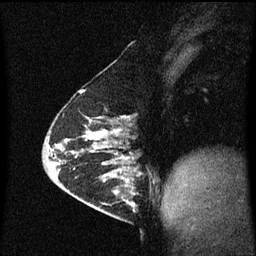
Breast MRI (dynamic contrast-enhanced), one sagittal slice; dynamic contrast-enhanced series, image 2 of 3 at this slice position (ordered by acquisition); 1.5 T; TE 4.2 ms, TR 8.4 ms; 2 mm slice thickness; 256 × 256 image matrix, field of view 200 × 200 mm. Female patient, age 63 years.
Structures marked on this image (semi-automatic segmentation, software-assisted and operator-edited):
- analysis volume of interest (the breast-tissue region the enhancement analysis was run in; not a lesion): box from (x=98, y=168) to (x=143, y=217) px
- tumour enhancement mask (voxels above the 70 % enhancement threshold inside the analysis volume of interest): (x=104, y=168)–(x=143, y=209)